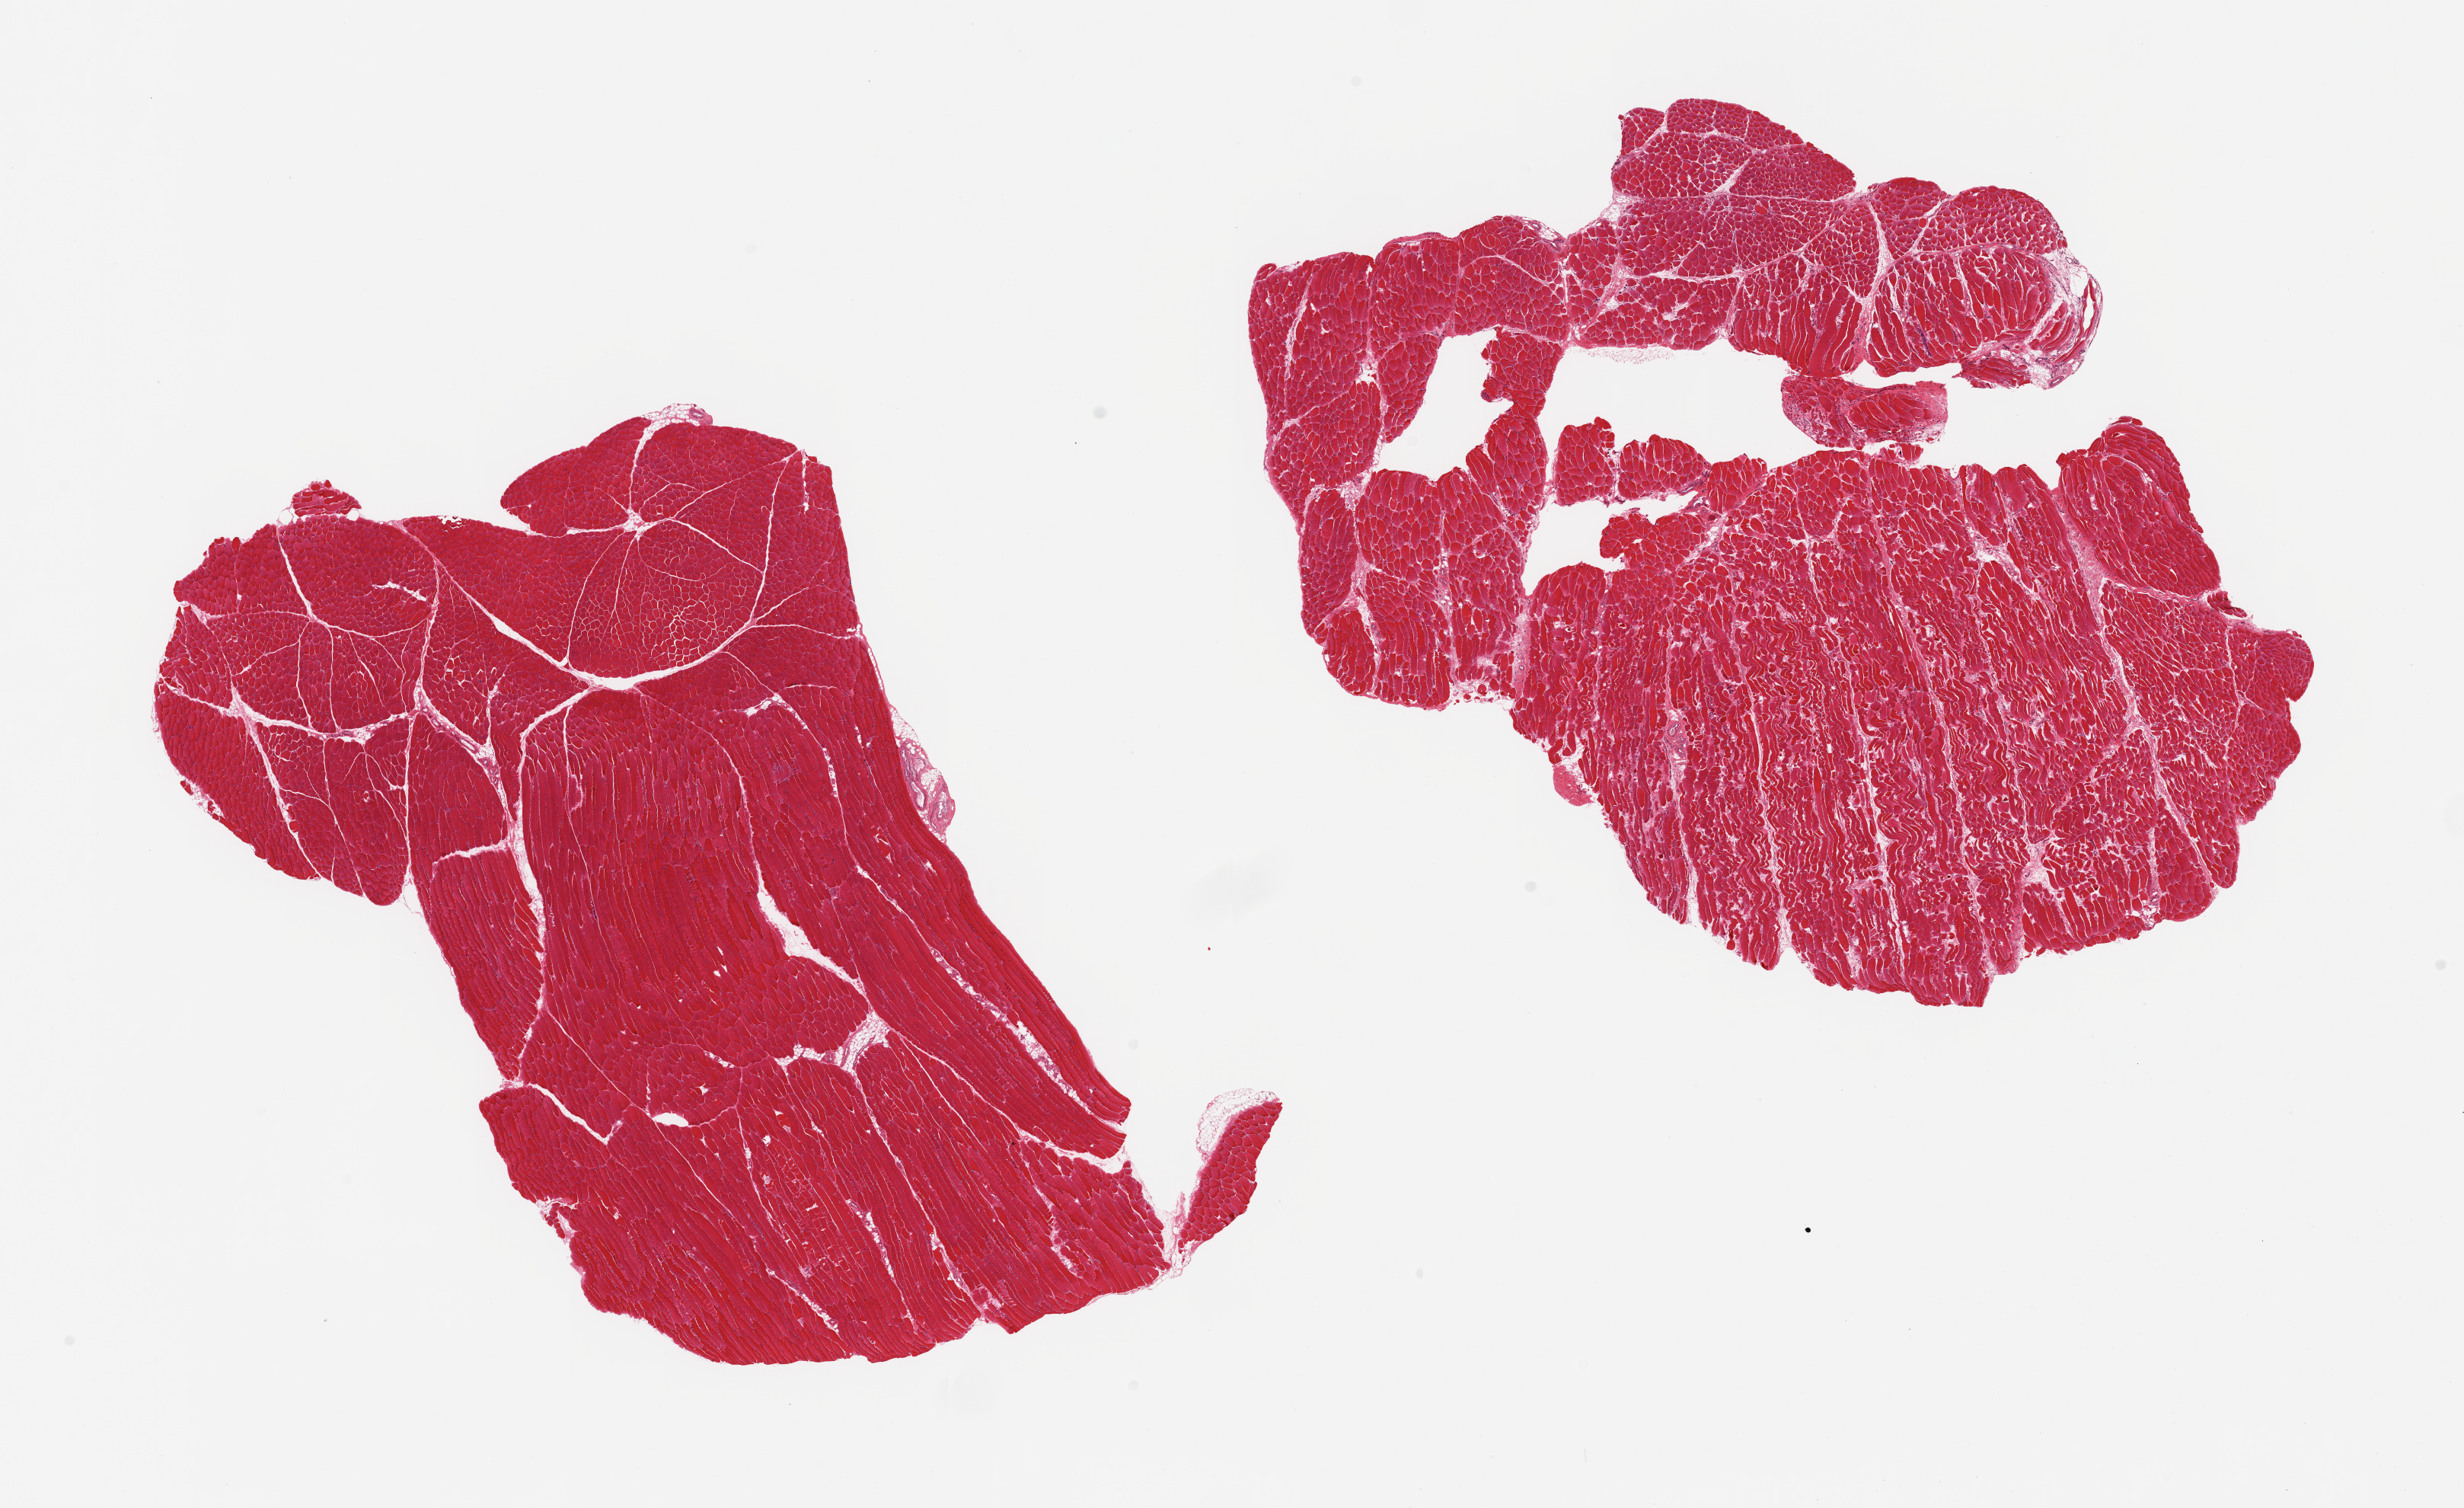
Whole-slide image, haematoxylin and eosin stain, low-resolution overview of the scanned area, about 25.6 x 15.7 mm (slide scanned at 20x); PAXgene-fixed, paraffin-embedded tissue; sampled site (target tissue): skeletal muscle; donor tissue sample. Donor: female.
* review note (as recorded): 2 pieces, ~10% interstitial fat